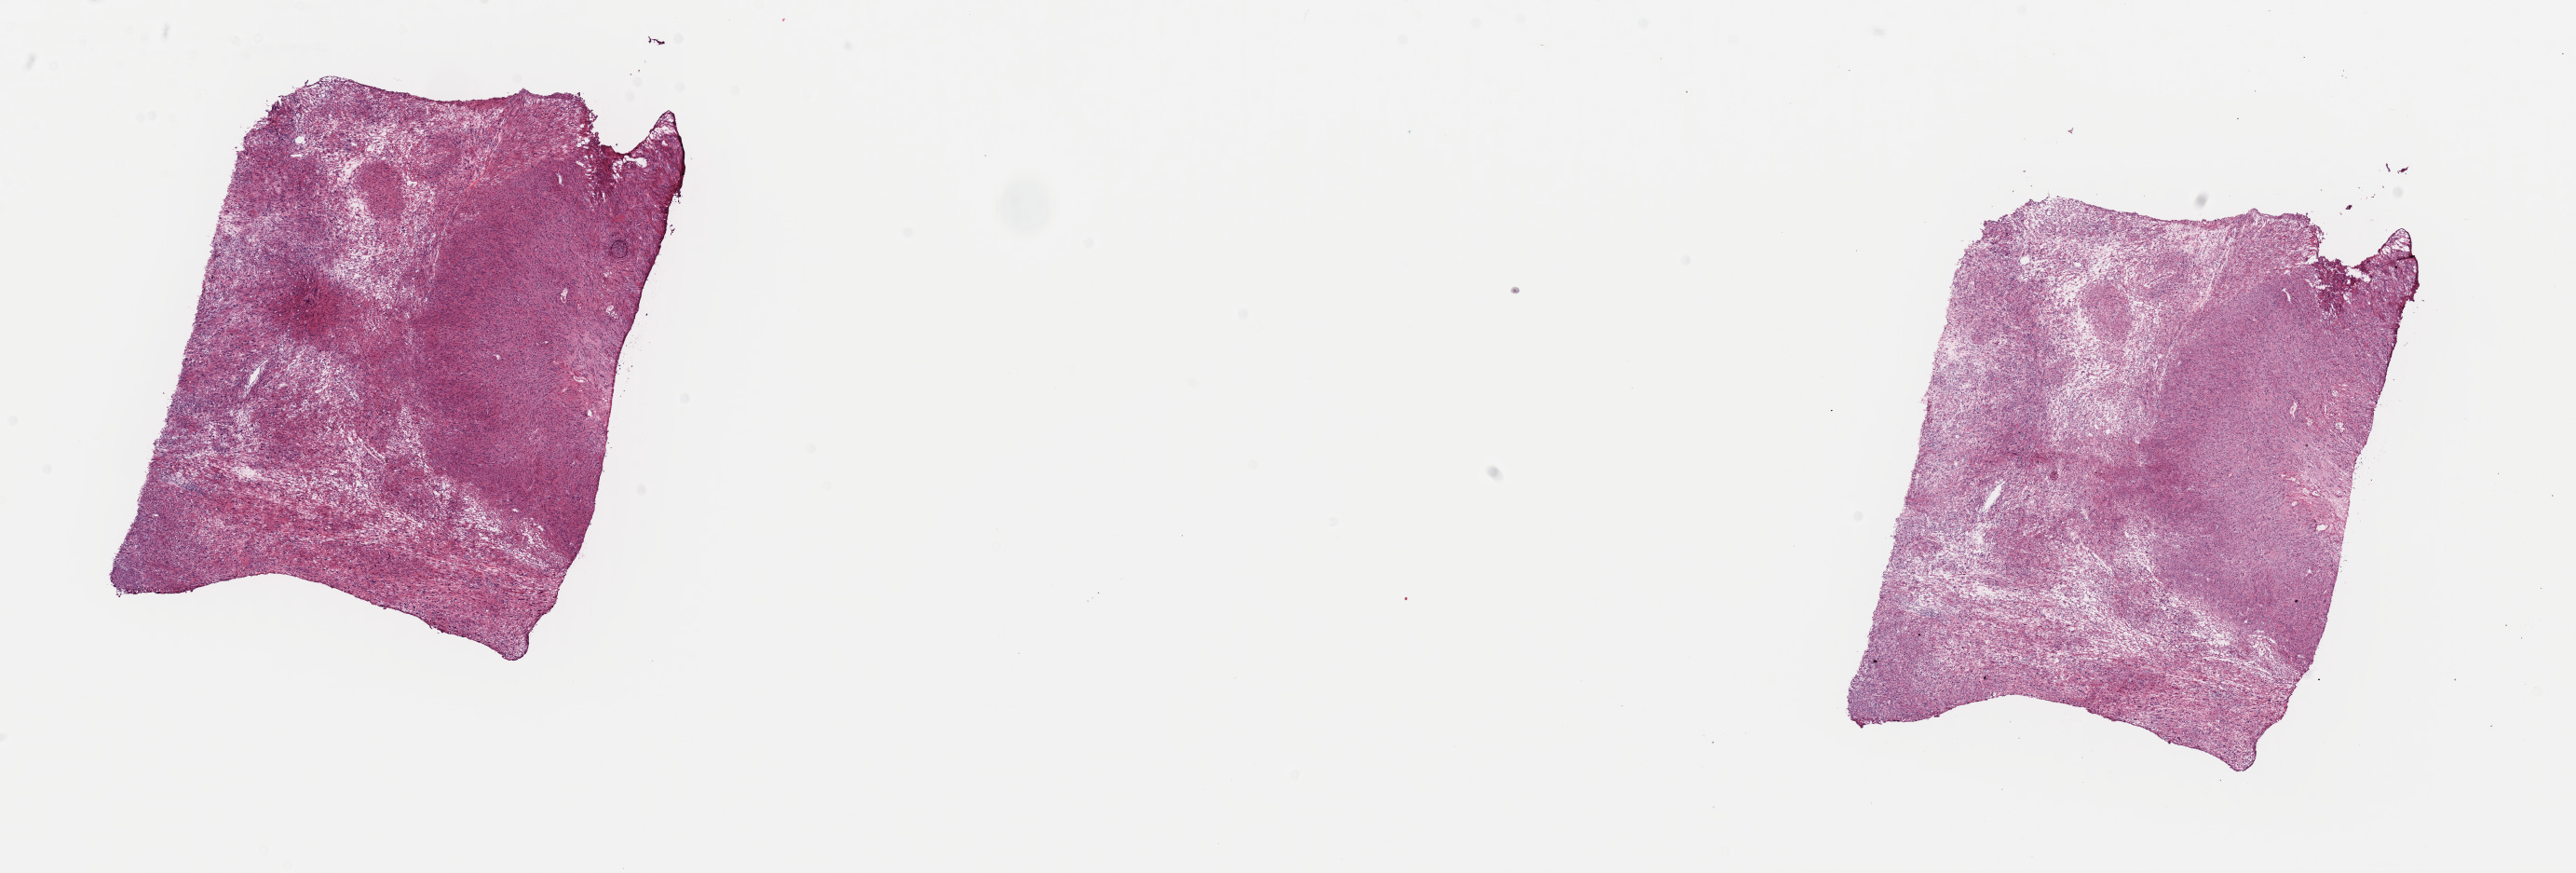
Digitized H&E-stained tissue section (whole slide) — whole scanned area (about 21.9 x 7.4 mm) shown as a low-resolution overview. Frozen section from the top of the tissue portion. Retroperitoneum and peritoneum, primary tumour sample. Female patient; age at initial diagnosis 56 years. Pathologist review of this section (percent, as recorded): tumour cells 100%, tumour nuclei 85%, normal cells 0%, stromal cells 0%, necrosis 0%. Infiltration values recorded for this section: lymphocyte infiltration 1%, monocyte infiltration 0%, neutrophil infiltration 0%.
Pathologic diagnosis: Leiomyosarcoma, NOS (retroperitoneum).